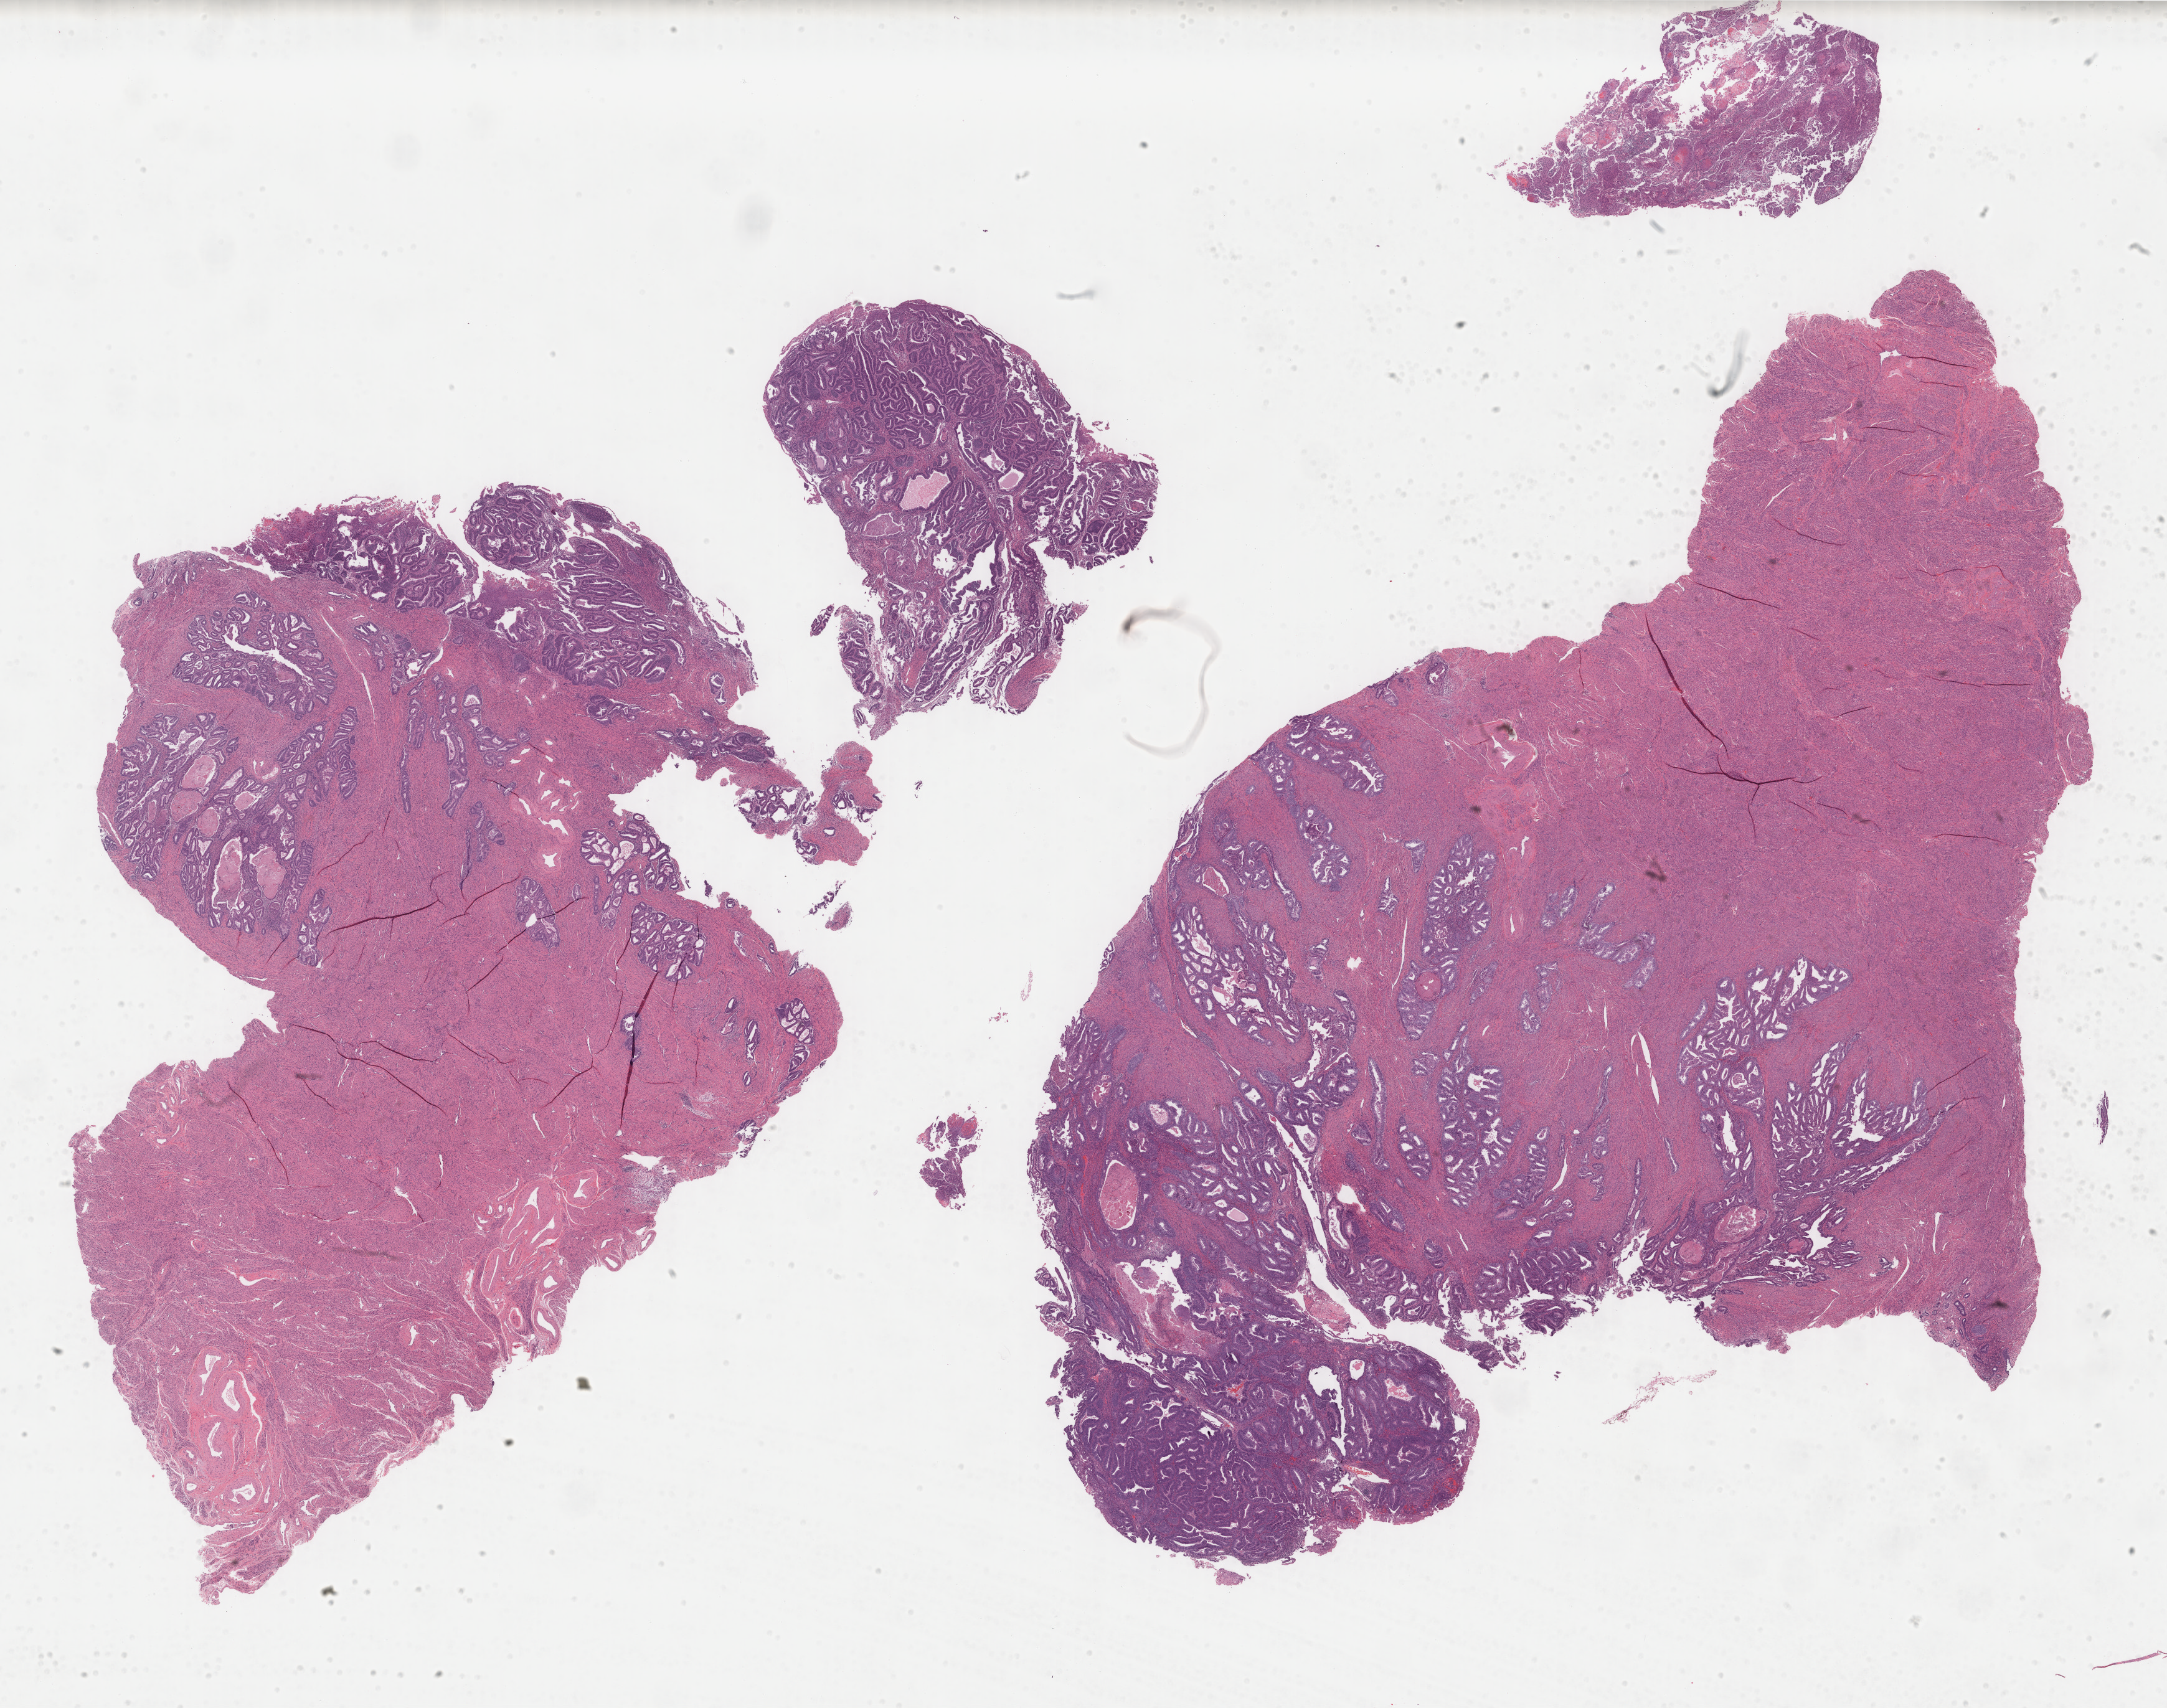
Digitized Hematoxylin and eosin (H&E) stained tissue section (whole slide) — whole scanned area (about 27.6 x 21.8 mm) shown as a low-resolution overview. Formalin-fixed paraffin-embedded (FFPE) diagnostic section. Uterus, primary tumour sample. Patient: female, age at initial diagnosis 64 years. Histologic grade: G2 (moderately differentiated).
Lymph nodes positive (case pathology): 0 of 18 examined. Diagnosis: Endometrioid adenocarcinoma, NOS (endometrium). FIGO stage: IC.